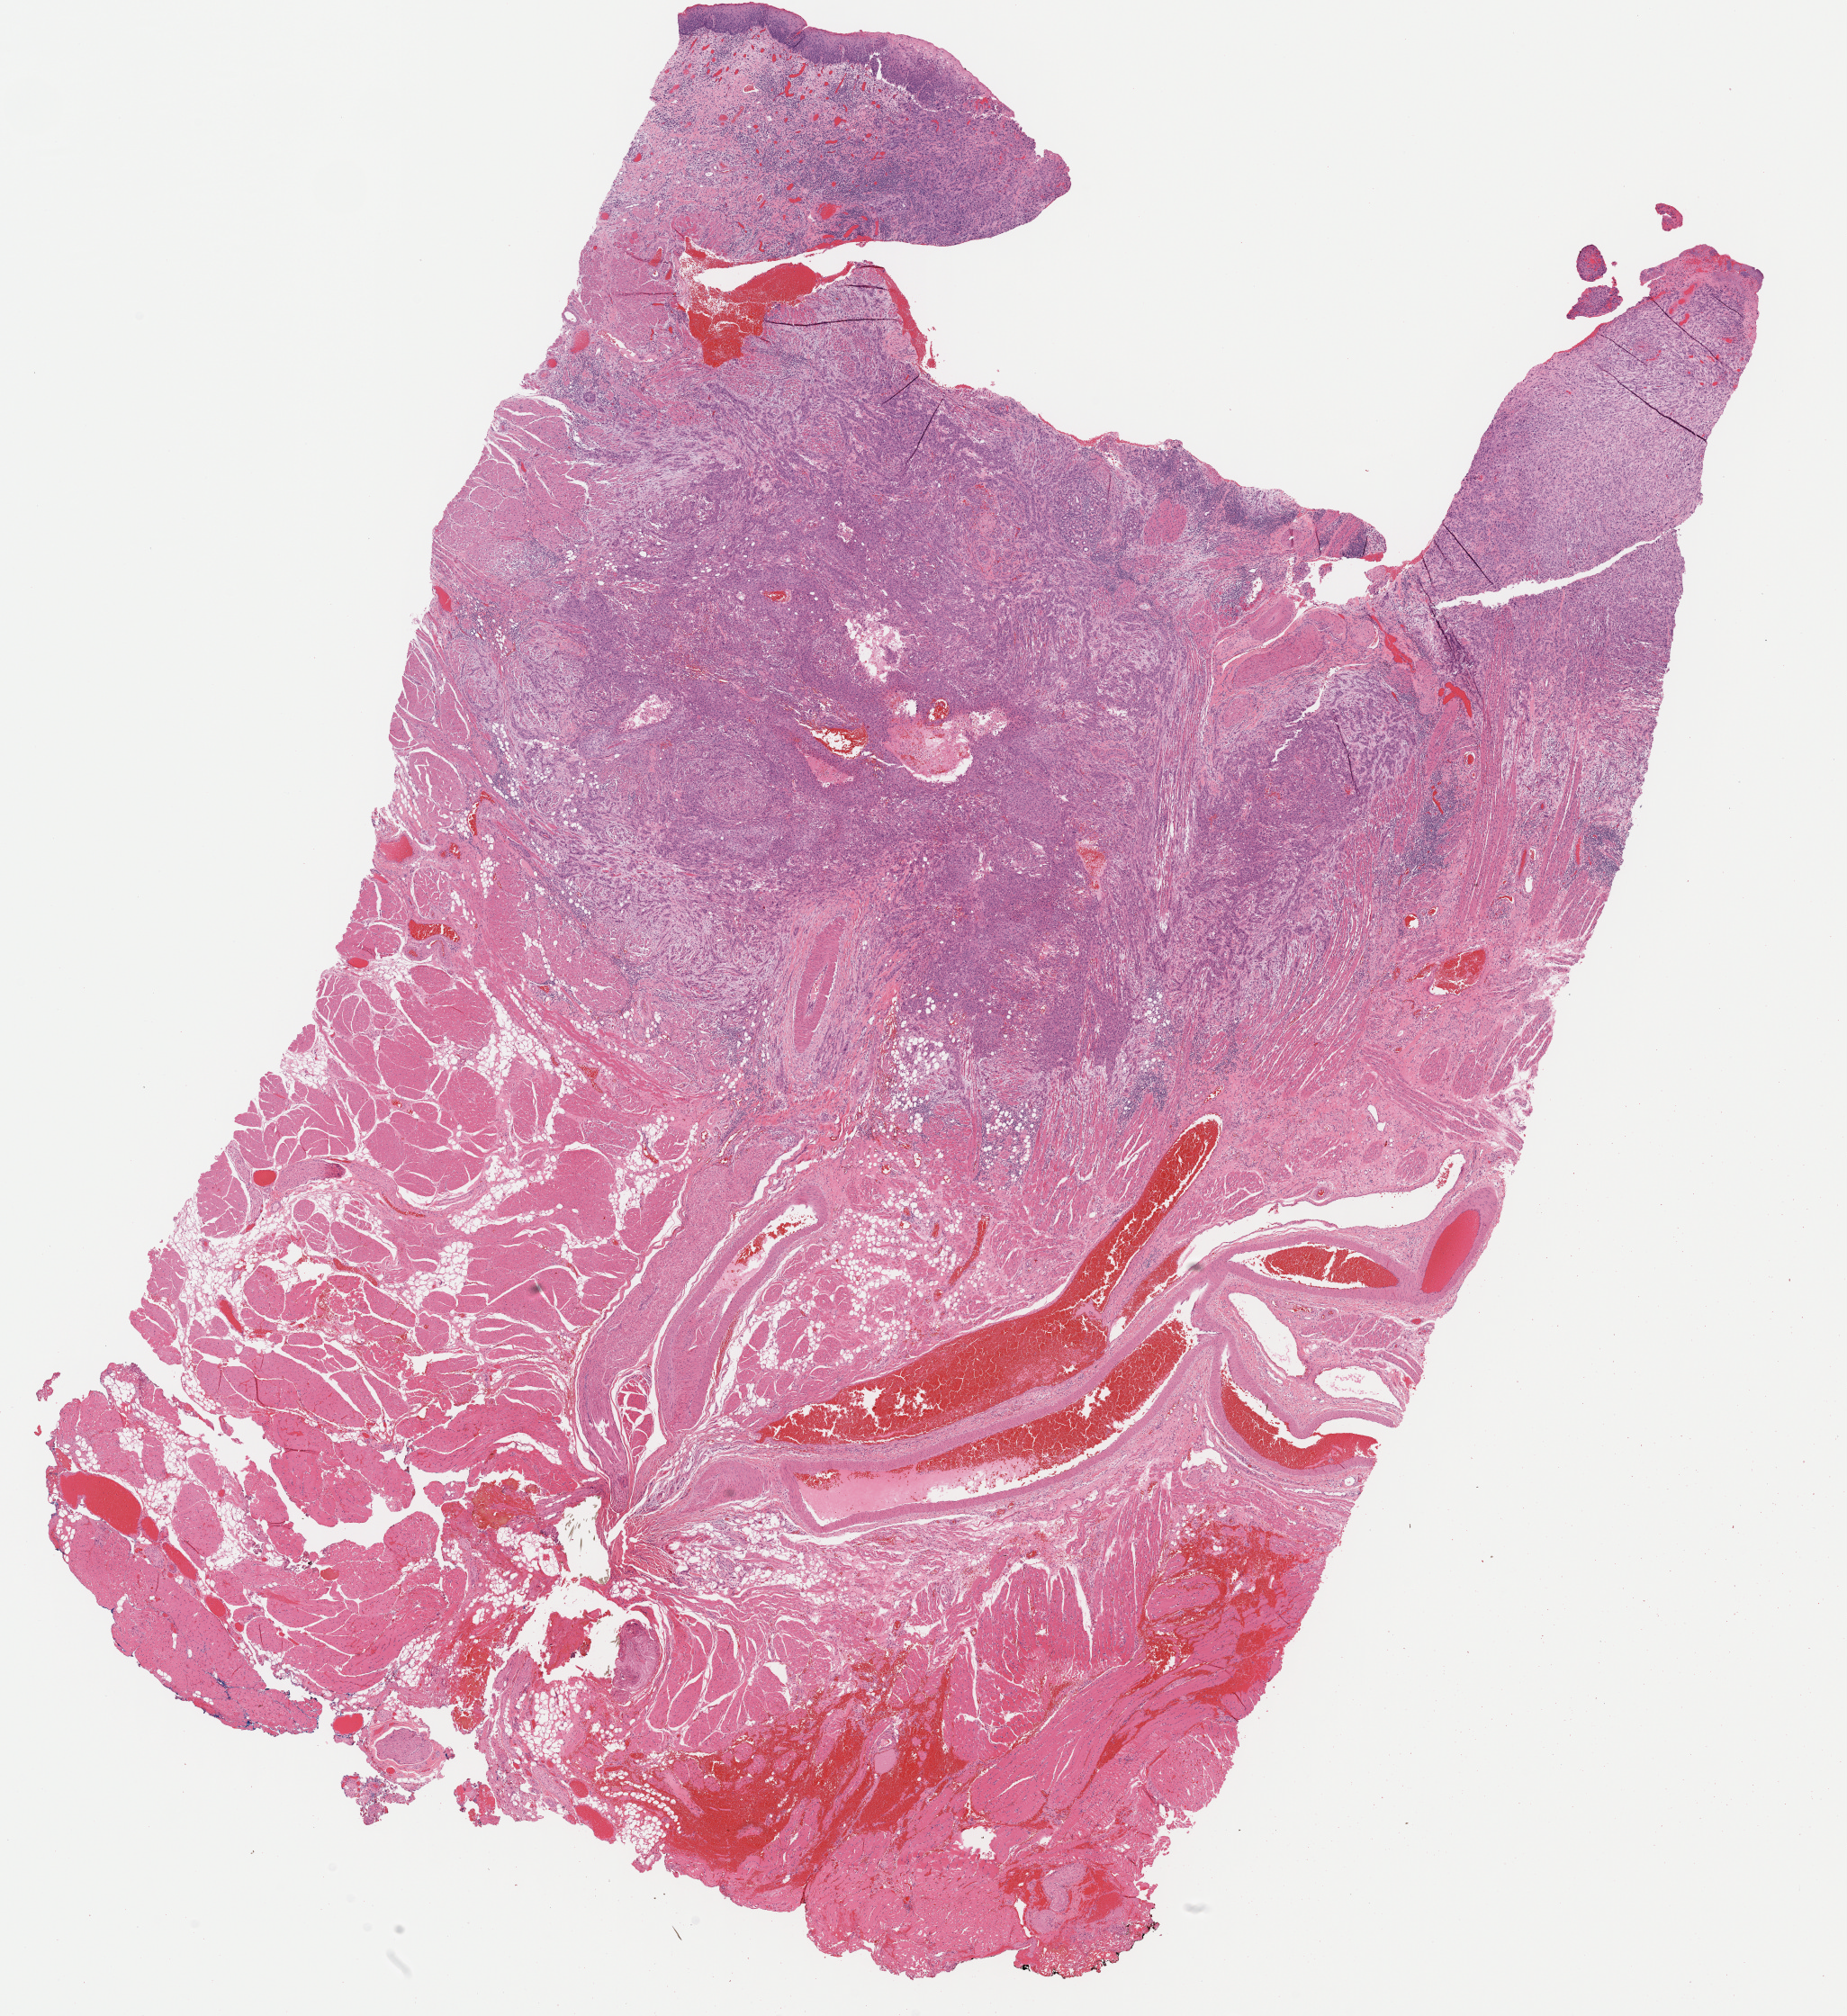
Whole-slide histology image, Hematoxylin and eosin (H&E) stained, a low-resolution overview of the entire scanned area, about 16.2 x 17.7 mm; FFPE section; primary tumour sample from the head and neck. Patient: male, age at initial diagnosis 41 years. Histologic grade: G3 (poorly differentiated).
Laterality: right. AJCC pathologic stage: I (6th edition). Histologic diagnosis: Squamous cell carcinoma, NOS (tongue, NOS).